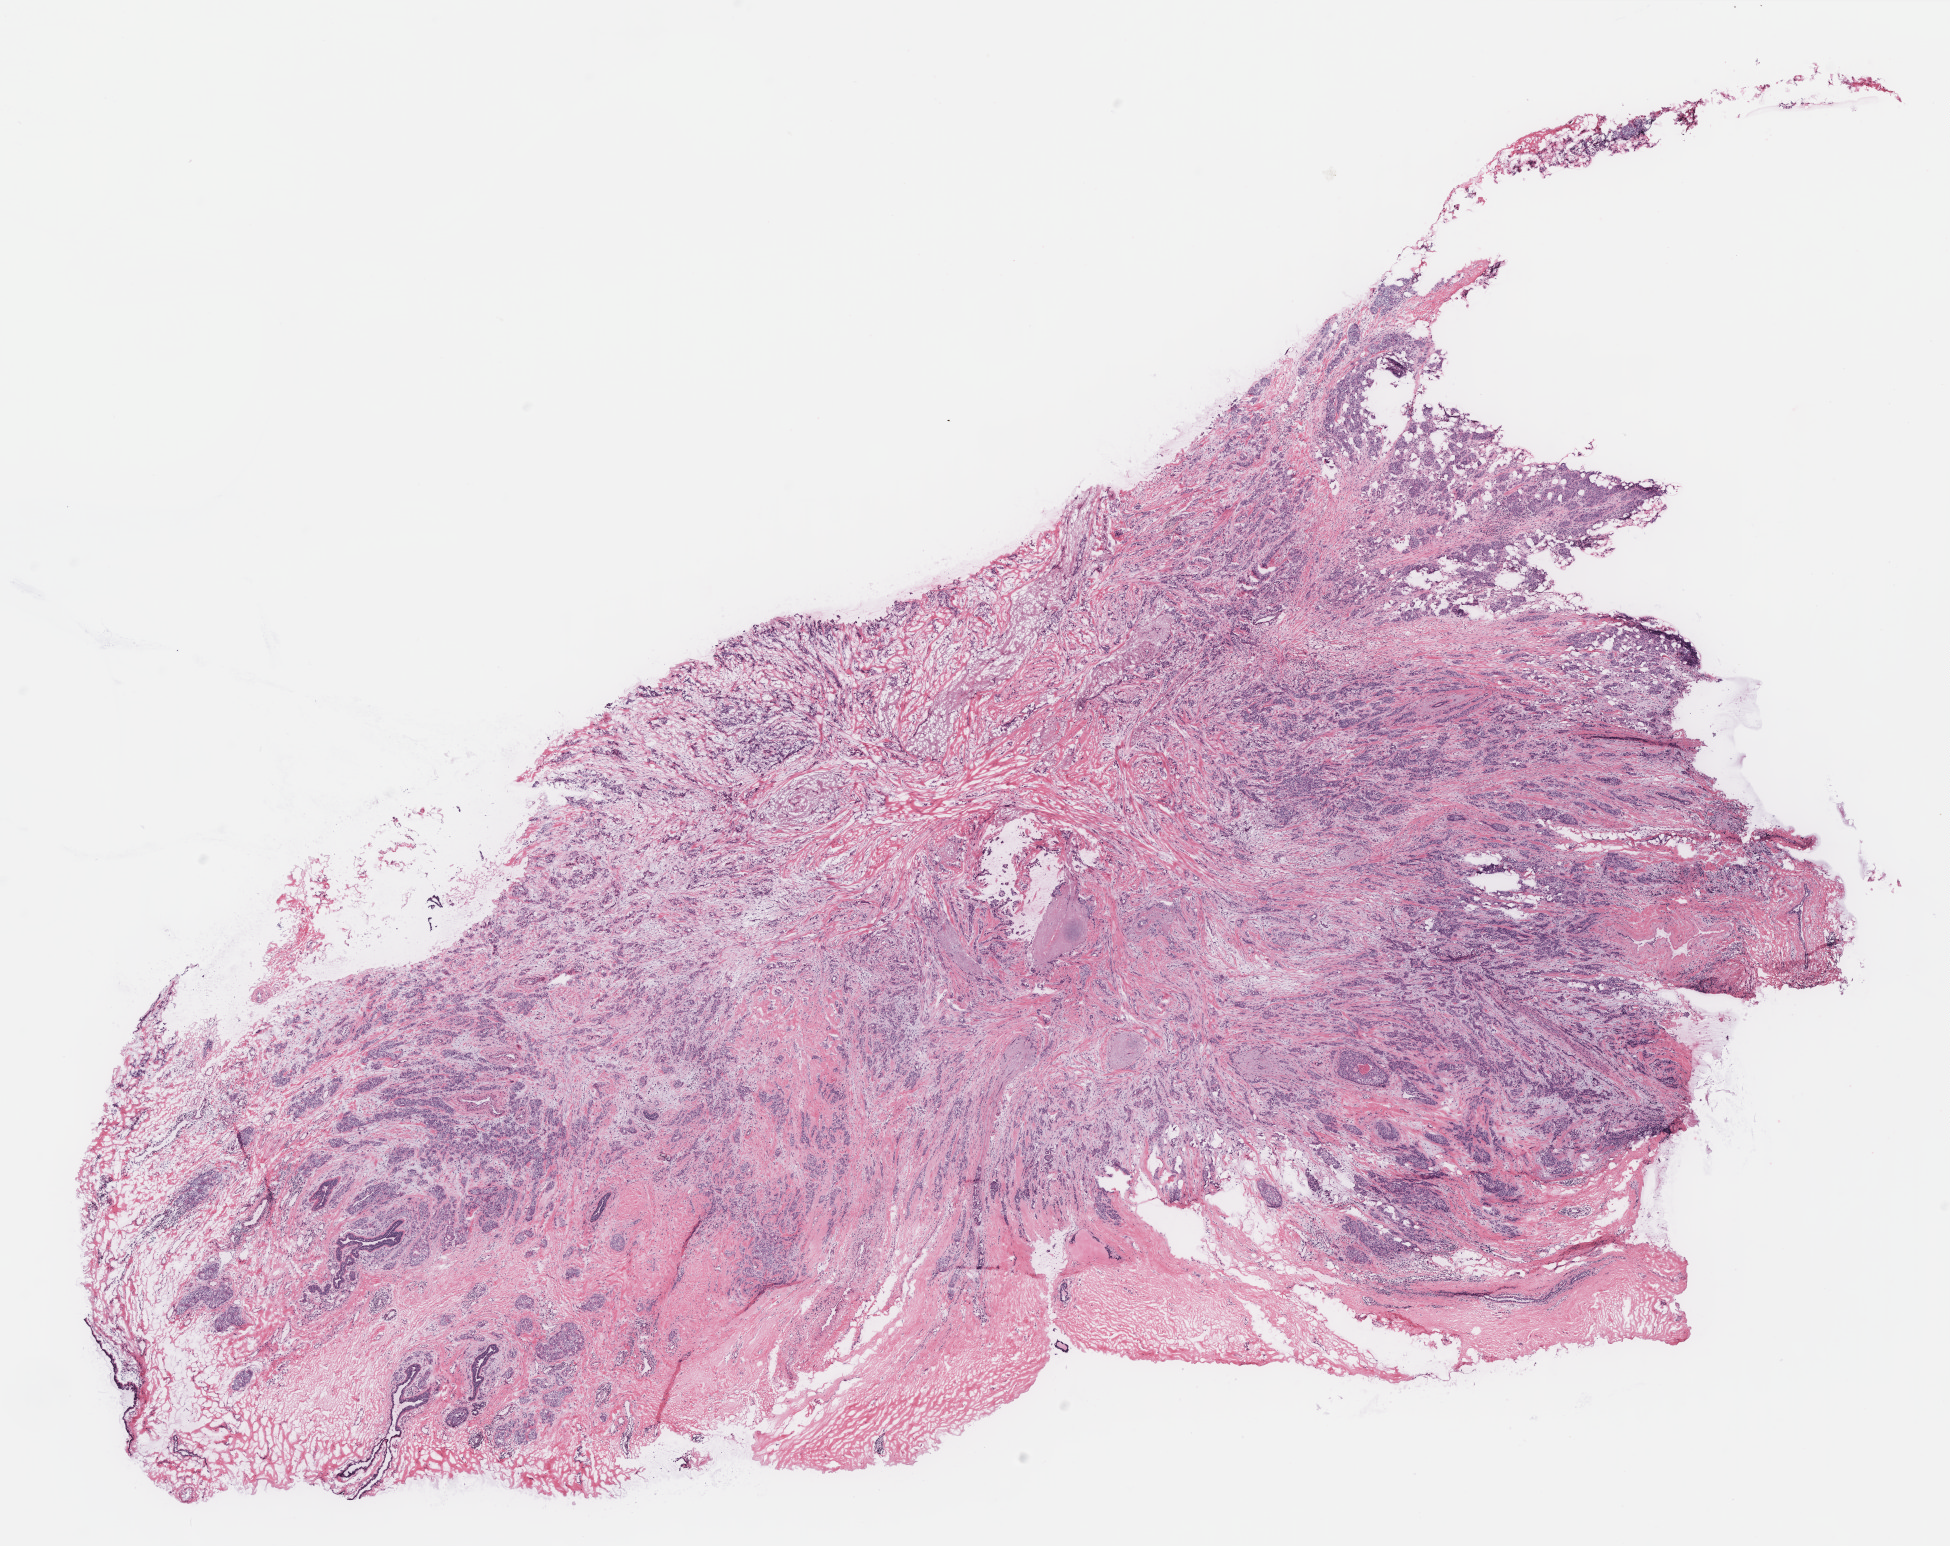
H&E-stained whole-slide image, whole scanned area (about 15.6 x 12.4 mm) shown as a low-resolution overview, breast, tissue type not recorded.
Patient diagnosis (cohort enrolment): breast cancer (breast).